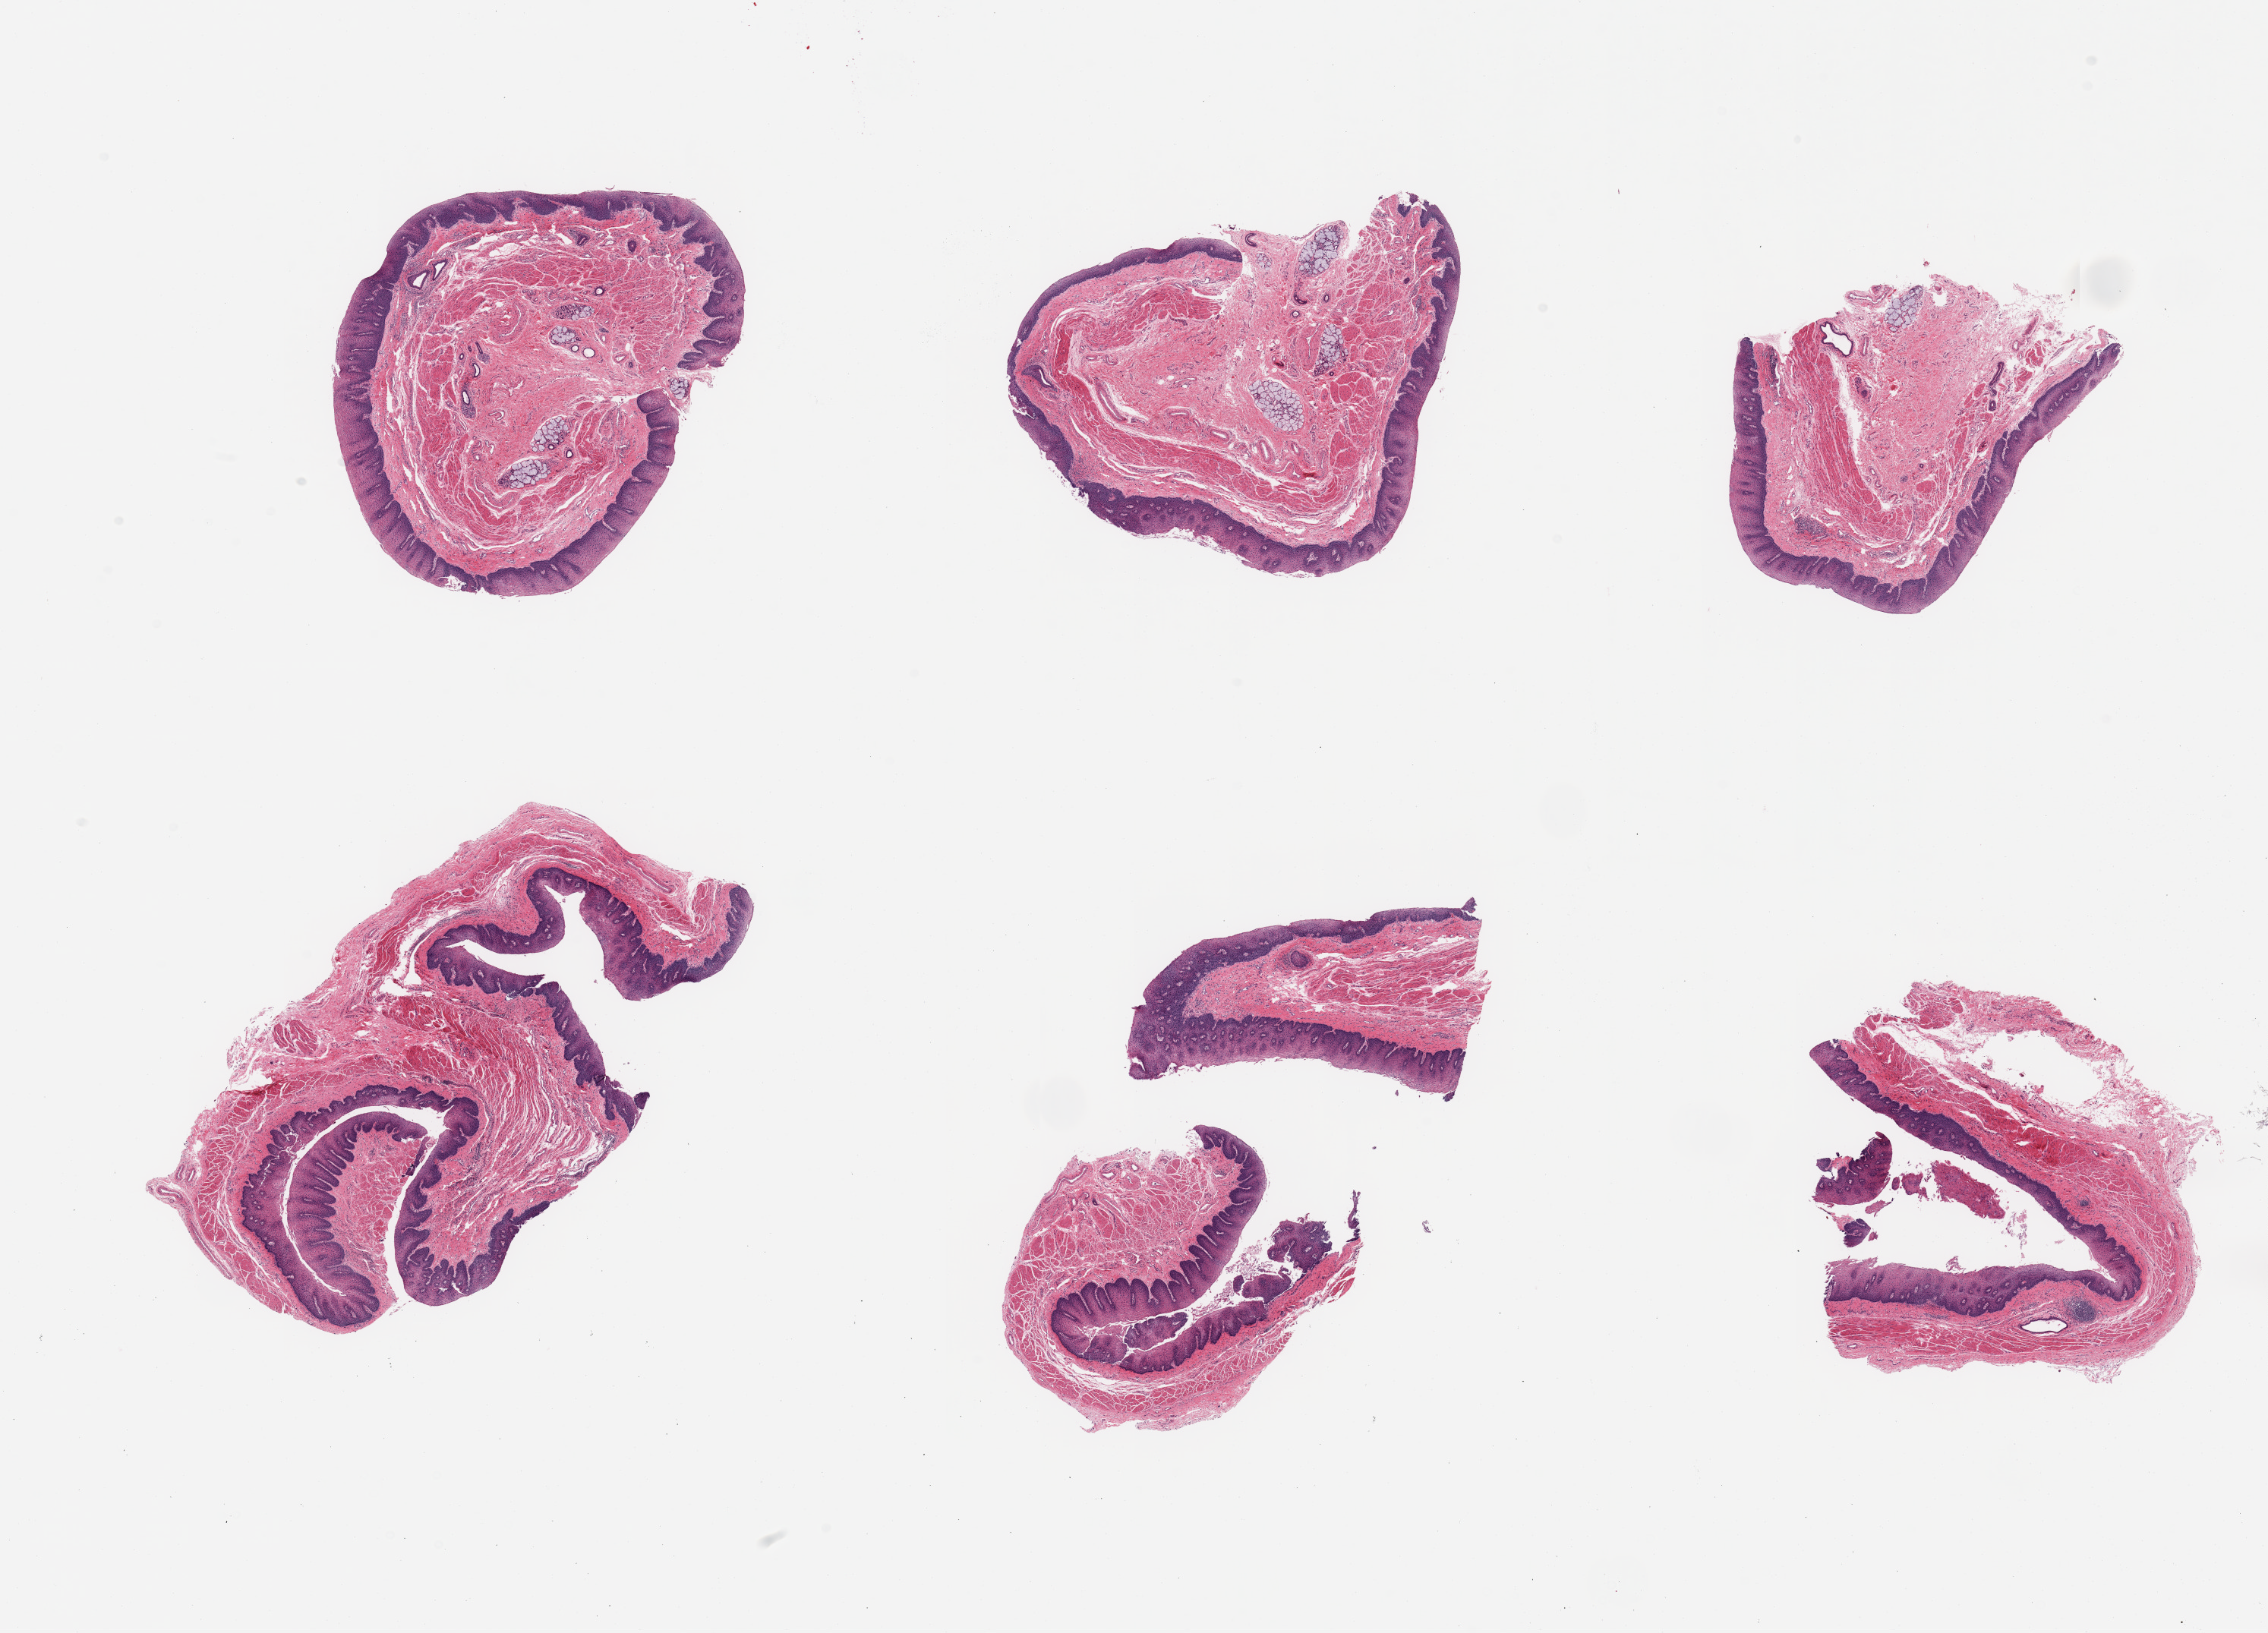
Hematoxylin and eosin (H&E) whole-slide image — a low-resolution overview of the entire scanned area, about 23.6 x 17.0 mm (from a 20x scan); PAXgene-fixed, paraffin-embedded tissue; section of esophageal mucous membrane (target tissue); donor tissue sample. Donor: female.
- reviewer comment on this tissue sample: 6 pieces (fragmented); focal inflammatory cells in epithelial layer